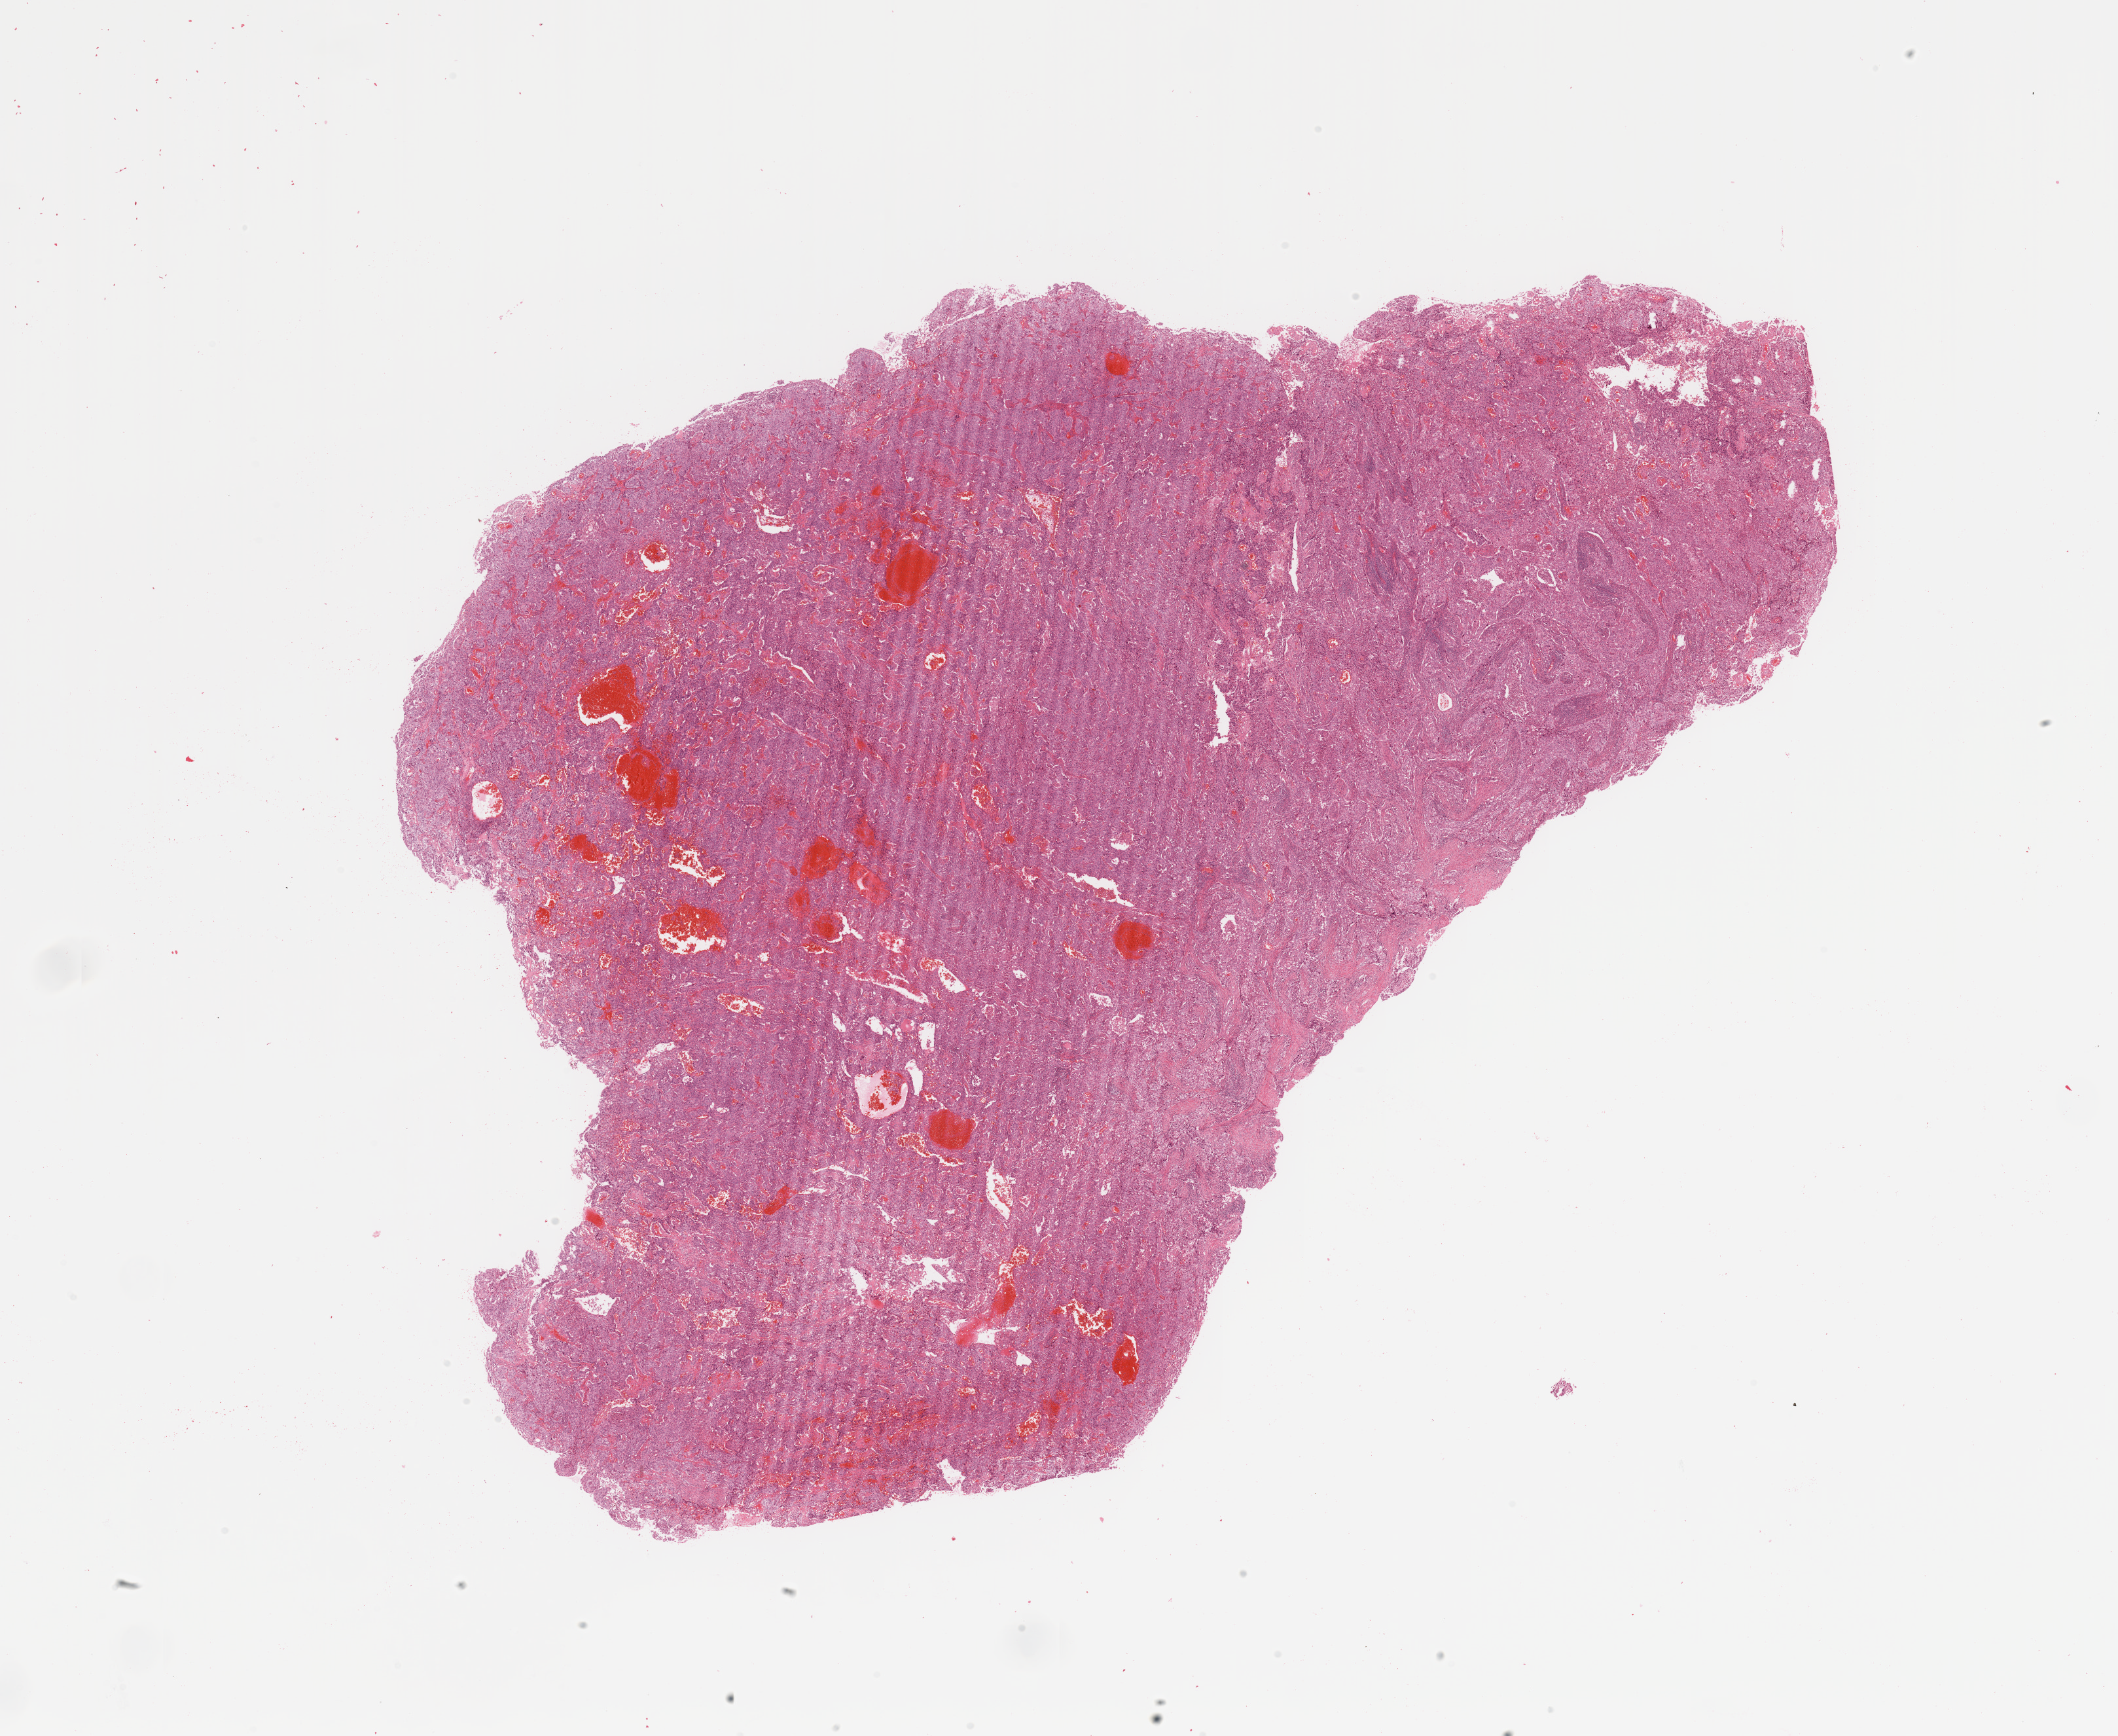
H&E-stained whole-slide image, whole scanned area (about 25.6 x 21.0 mm) shown as a low-resolution overview. Tumour tissue sample, sampled site: lung. Patient: male, age 60 years. Composition of this section per pathologist review: tumour nuclei 80%, necrosis 3%.
Diagnosis: Adenocarcinoma, NOS.